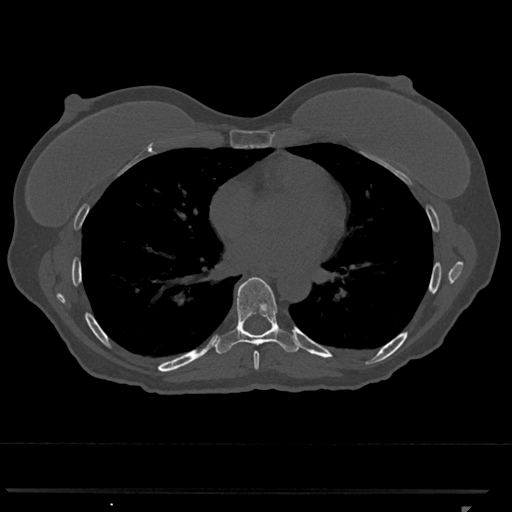
CT including the spine, one axial slice. Slice 672 of 793 in the series (ordered by position). Reconstruction kernel Br40s/3. Bone window (W 1800 / L 400 HU). 0.5 mm slice thickness. 512 × 512 image matrix, field of view 380 × 380 mm. Patient: female, 62 years. Case-level facts recorded for this patient, not image findings: primary cancer: renal.
Outlined on this slice (semi-automatically segmented with operator editing):
- T7 vertebra: box from (x=253, y=351) to (x=259, y=370) px
- T8 vertebra: (x=214, y=277)–(x=299, y=354)